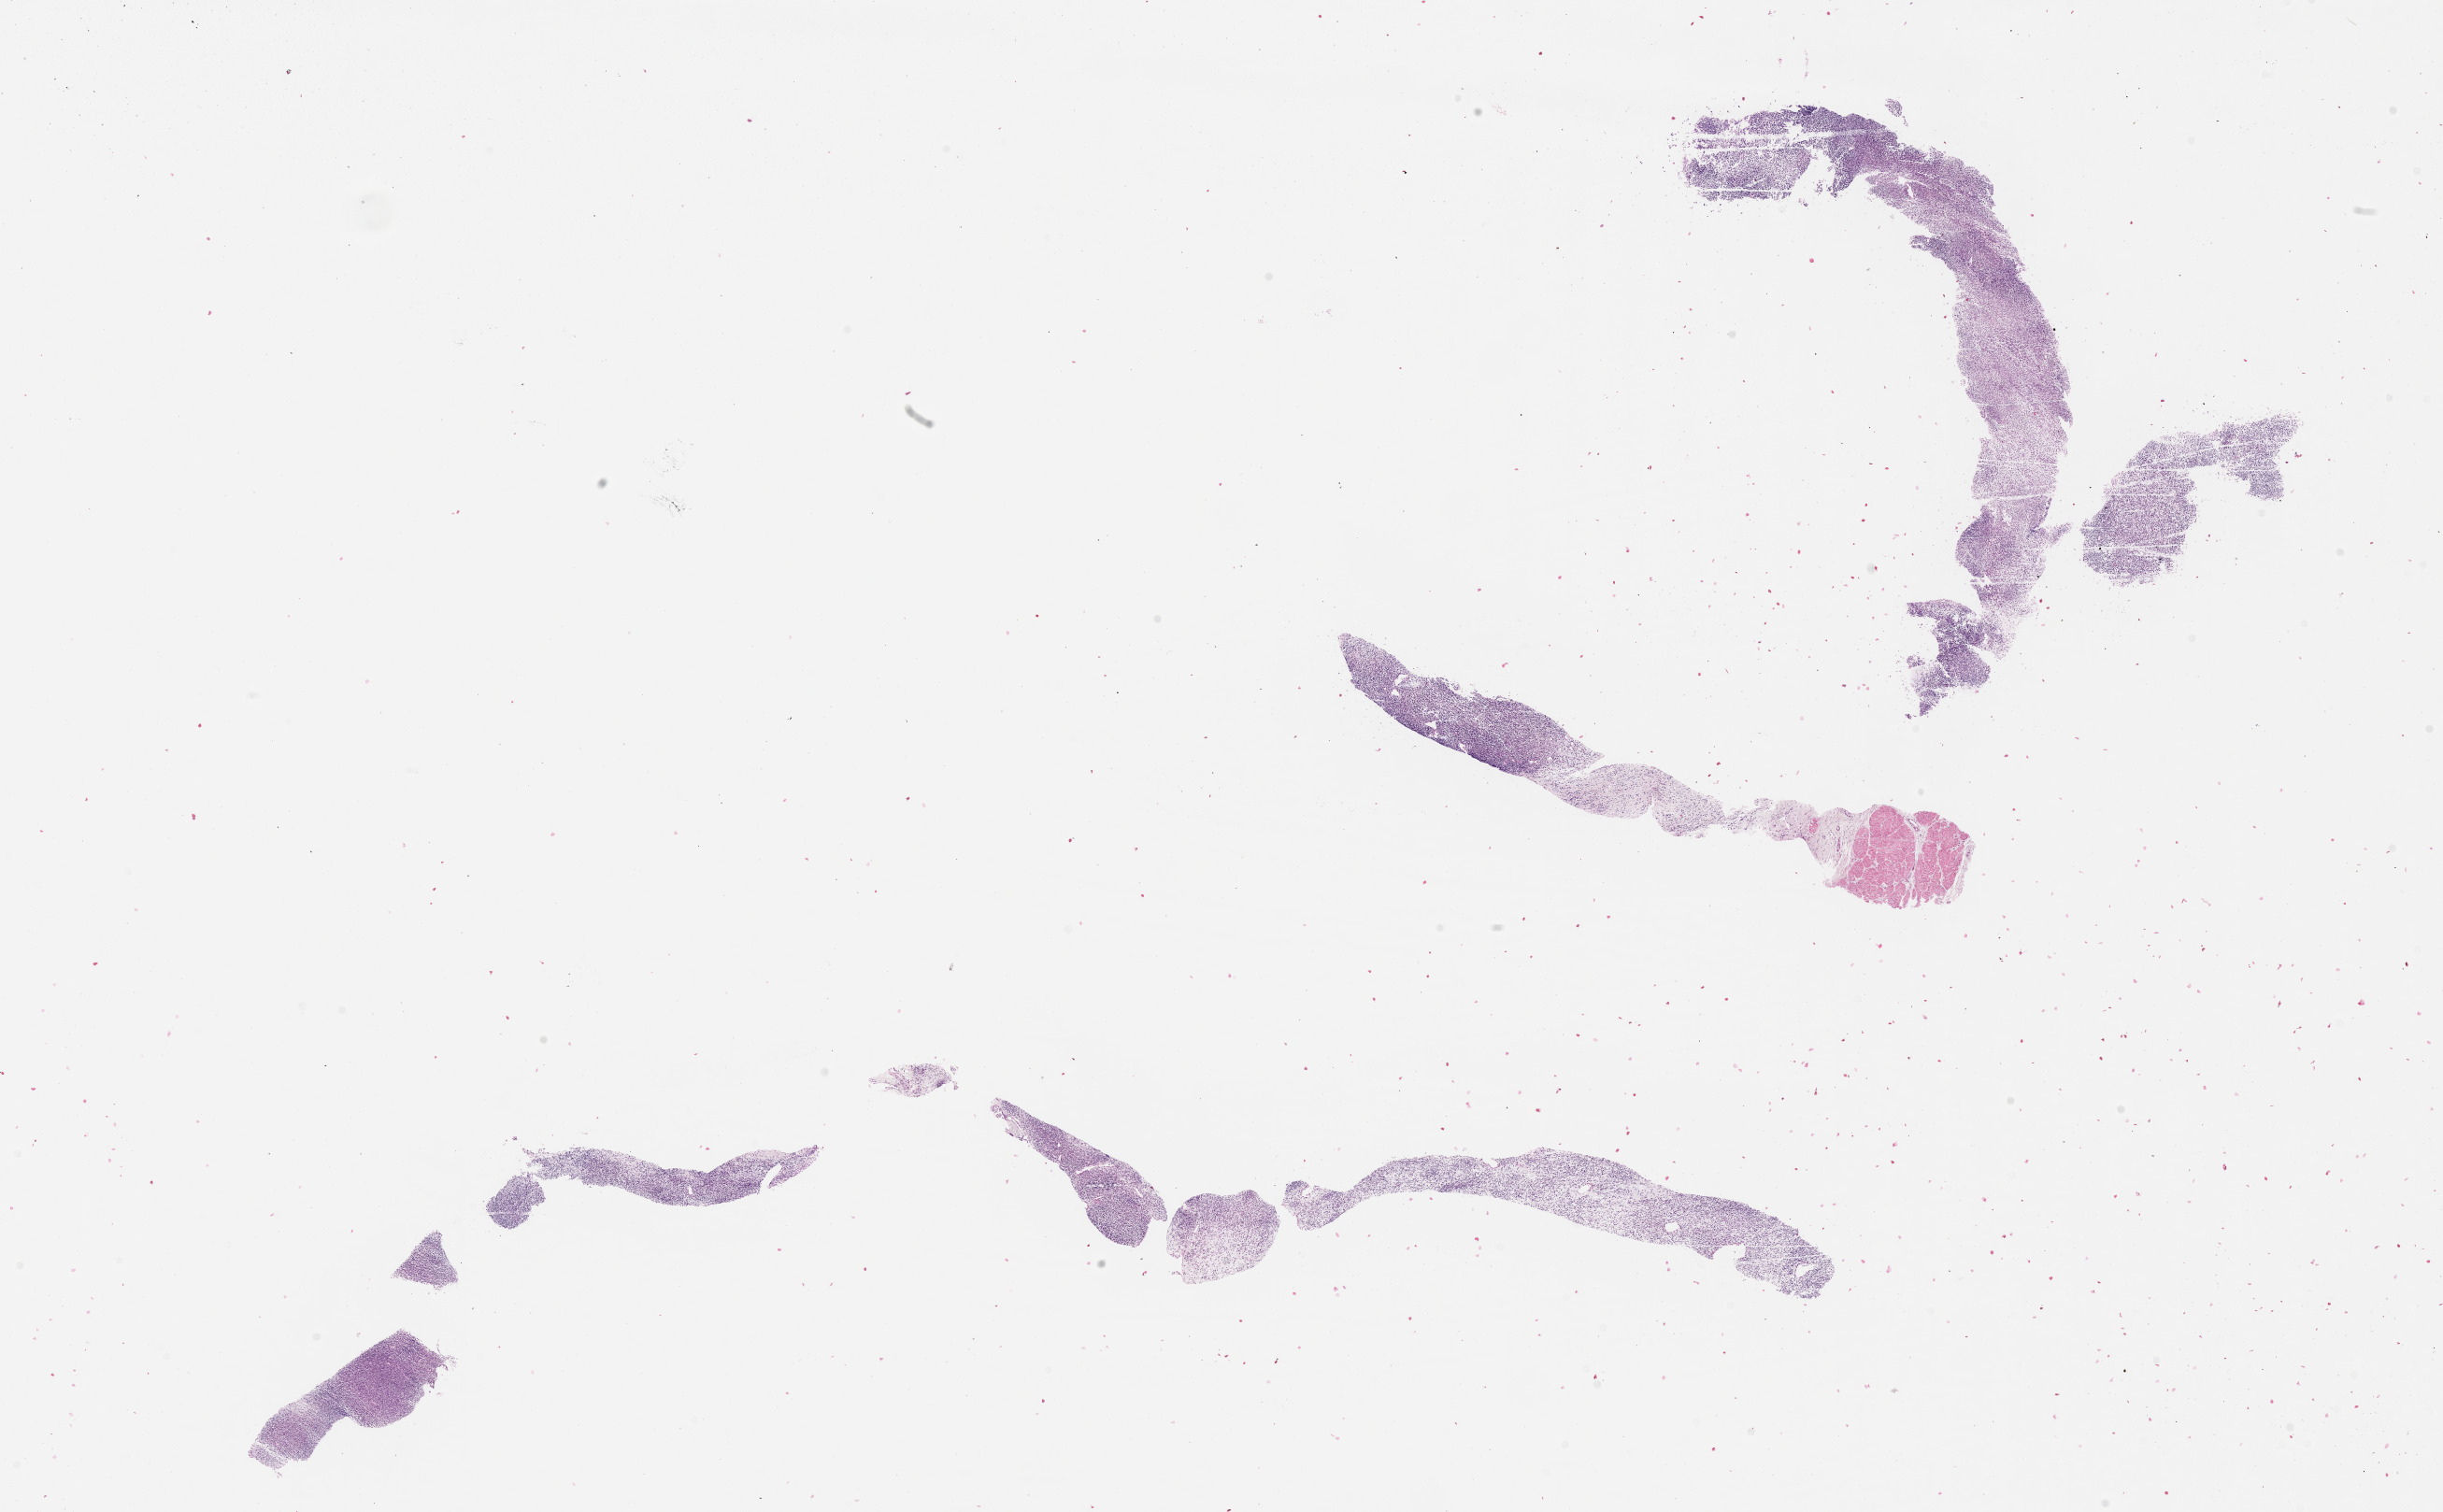
Digitized H&E-stained section of tumor tissue, low-resolution overview of the scanned area, about 21.1 x 13.1 mm, formalin-fixed paraffin-embedded section, sample anatomic site: pelvis. Male patient, age at diagnosis 3.1 years.
* metastatic status at presentation (as recorded): non-metastatic
* diagnosis: rhabdomyosarcoma; histological classification: embryonal rhabdomyosarcoma
* stage (as recorded): 3